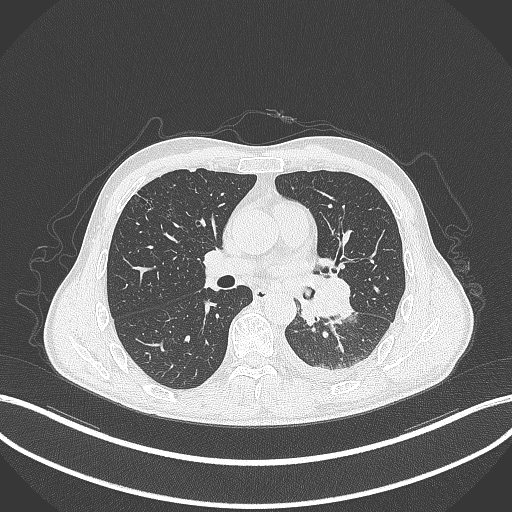
Chest CT, one axial slice; slice 174 of 295 in the series (ordered by position); reconstruction kernel B70f; lung window (W 1500 / L -600 HU); 1 mm slice thickness; 512 × 512 image matrix, field of view 400 × 400 mm. Male patient, age 47 years. From the clinical record (not read from this slice): clinical TNM (as recorded): T3 N1 M1c.
Annotated regions visible in this slice (rectangle marked by the reading radiologist):
- lung tumour (recorded histology: small cell carcinoma): bounding box (x1, y1, x2, y2) in pixels: (300, 277, 354, 327)